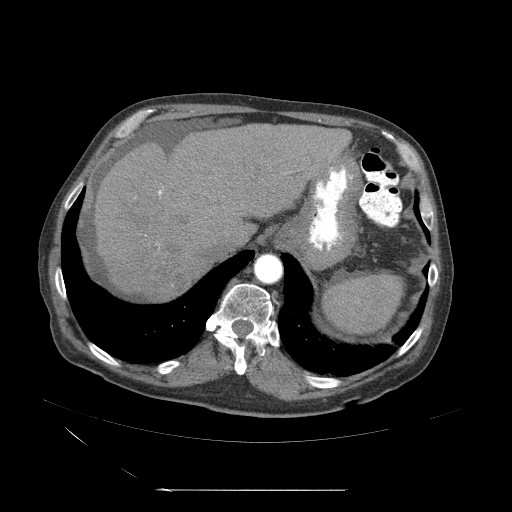
Contrast-enhanced abdominal CT (liver protocol), one axial slice. Slice 43 of 71 in the series (ordered by position). Soft-tissue window (W 400 / L 40 HU). 2.5 mm slice thickness. 512 × 512 image matrix. From the clinical record (not read from this slice): diagnosis: hepatocellular carcinoma (patient treated with transarterial chemoembolisation; whether this scan precedes or follows treatment is not stated here); TNM stage (as recorded): Stage-II; Child-Pugh class: A.
Structures marked on this image (semi-automatic segmentation, software-assisted and operator-edited):
- abdominal aorta: box from (x=254, y=254) to (x=284, y=285) px
- liver parenchyma outside the tumour (the mass and vessels are separate outlines, so this box may not span the whole liver): (x=91, y=125)–(x=354, y=306)
- mass: (x=147, y=266)–(x=189, y=306)
- liver vessels: (x=111, y=199)–(x=229, y=267)